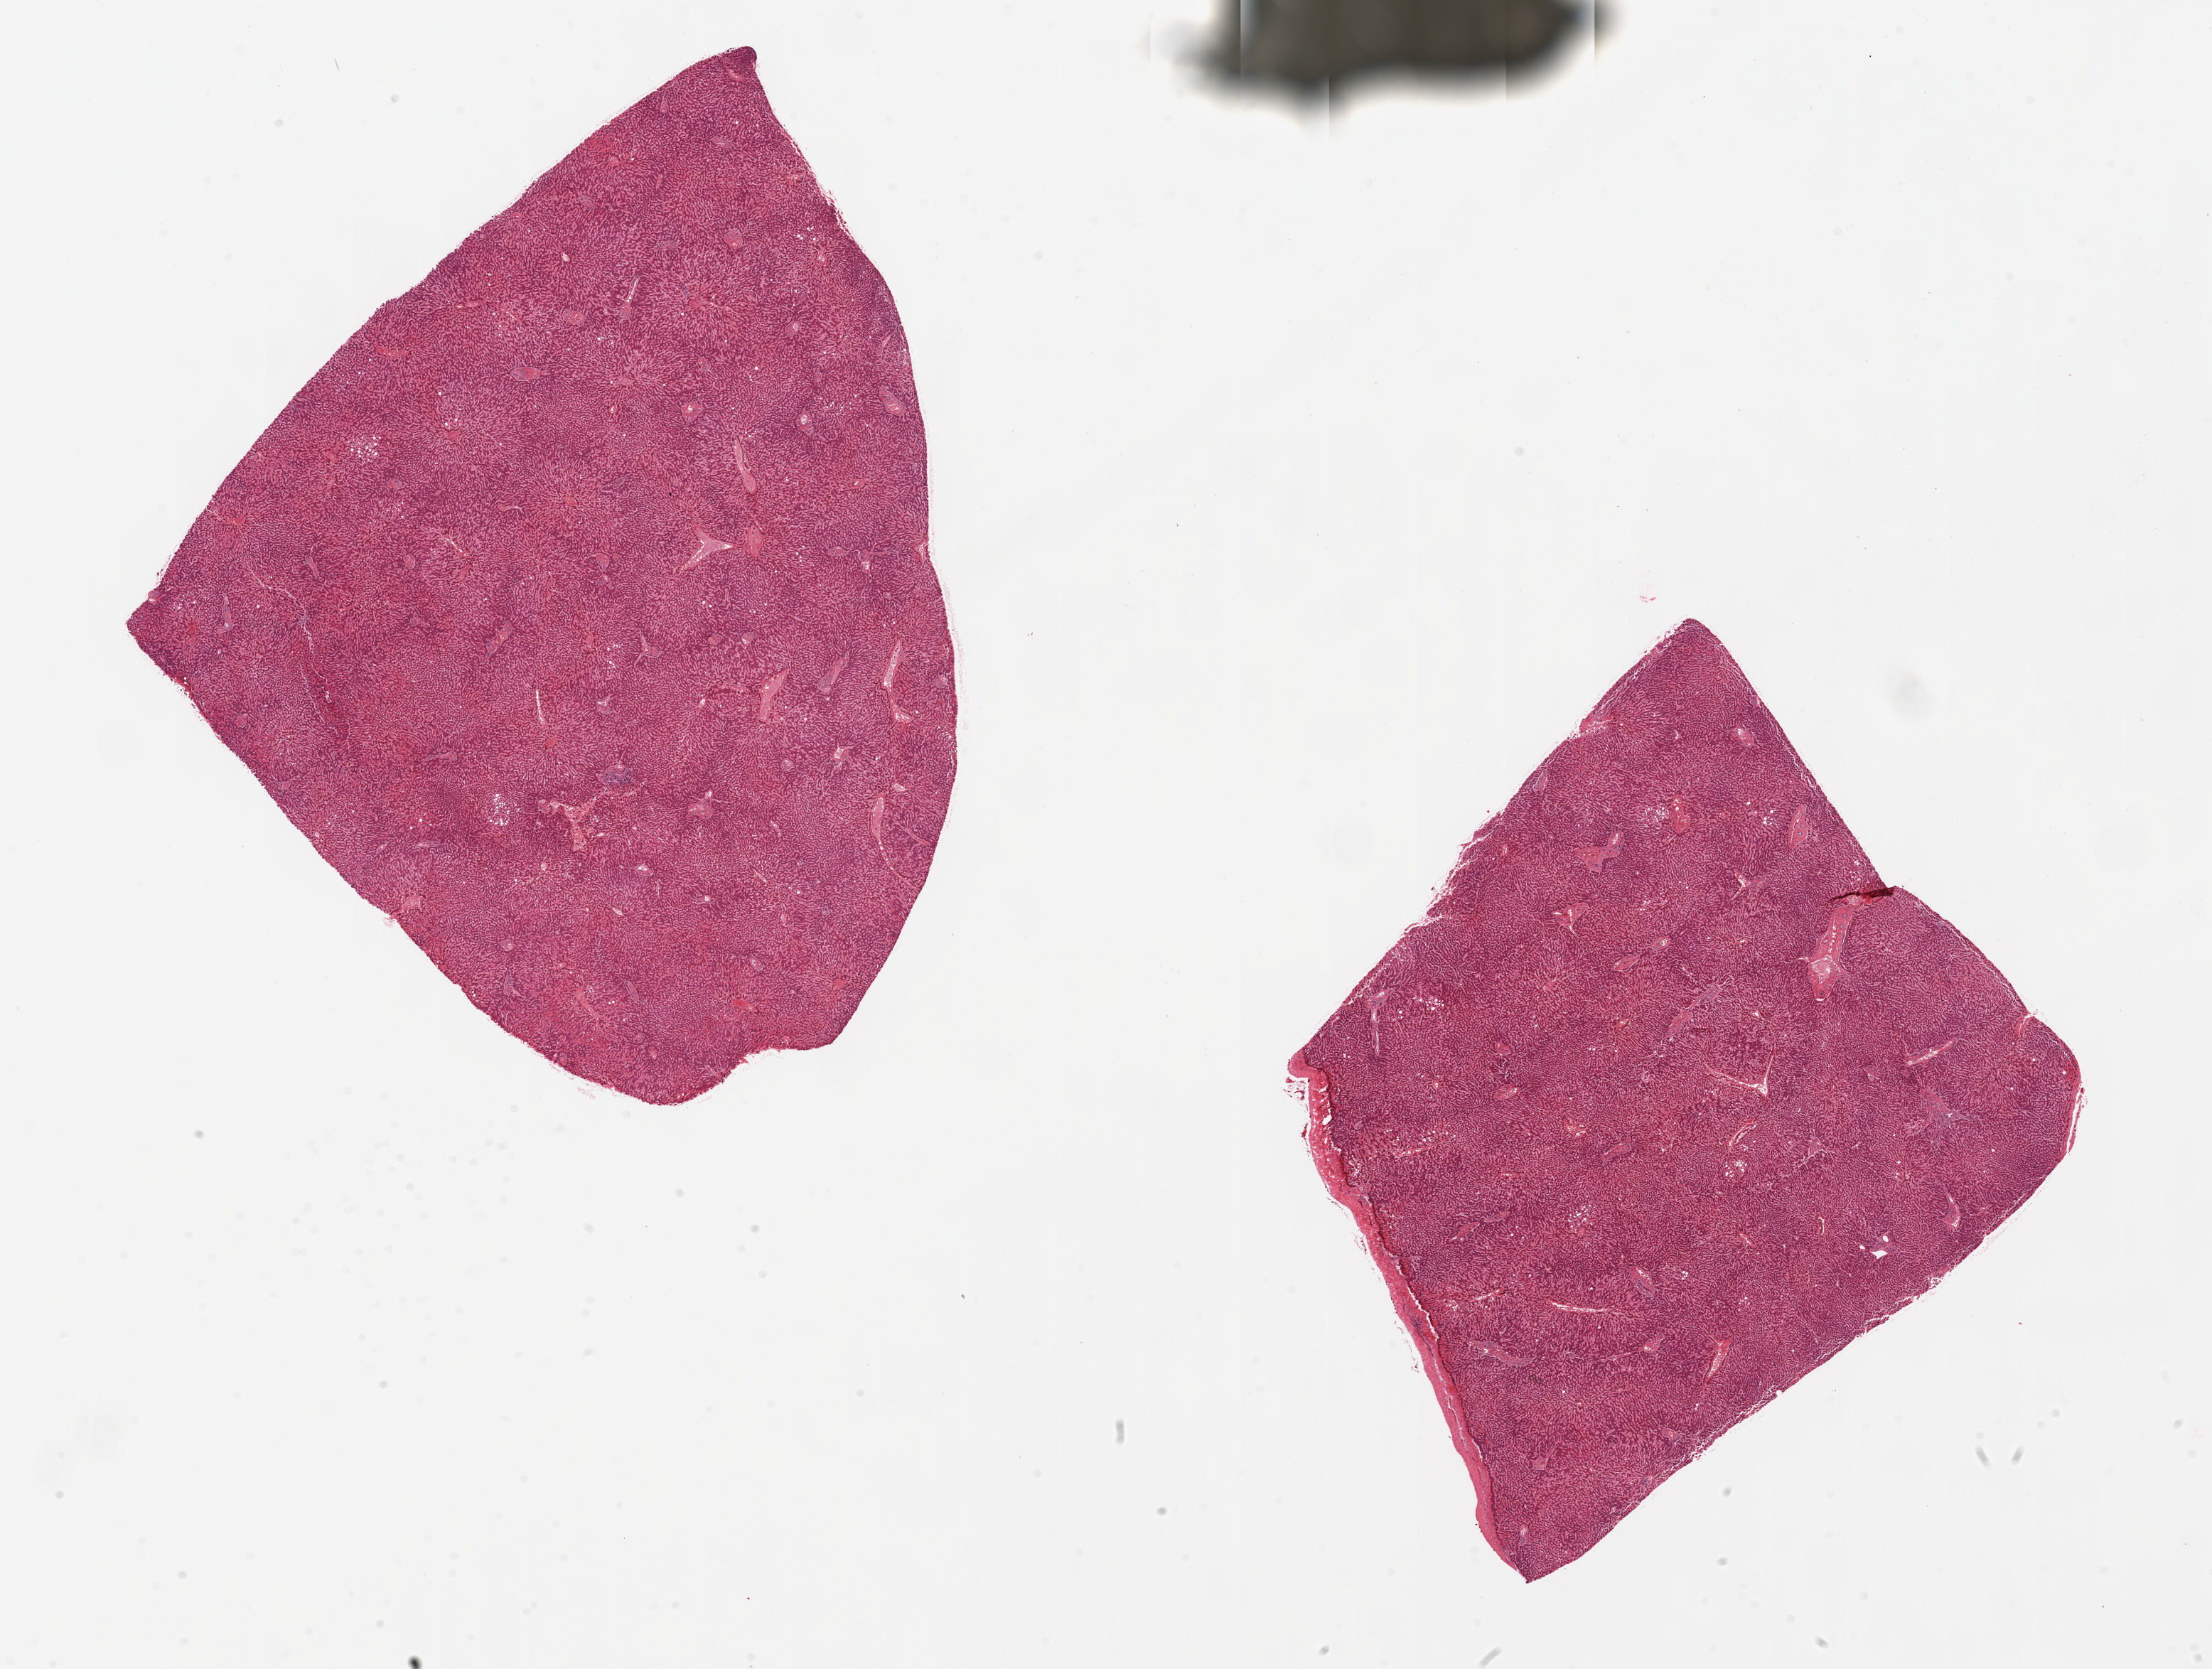
Hematoxylin and eosin (H&E) whole-slide image — a low-resolution overview of the entire scanned area, about 24.6 x 18.6 mm, PAXgene-fixed, paraffin-embedded tissue, sampled site (target tissue): liver, tissue donor sample.
Review note (as recorded): 2 pieces; <5% macrovesicular steatosis; no active or chronic lesions.